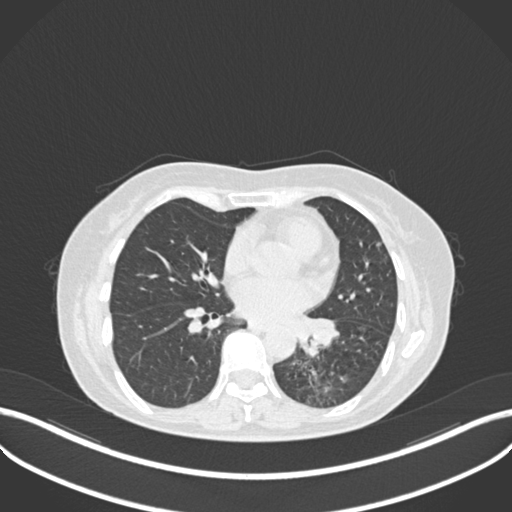
Chest CT, one axial slice; slice 120 of 270 in the series (ordered by position); reconstruction kernel B30f; 120 kVp; lung window (W 1500 / L -600 HU); 1 mm slice thickness; 512 × 512 image matrix, field of view 400 × 400 mm. Patient: female, 63 years. From the clinical record (not read from this slice): clinical TNM (as recorded): T1b N0 M0; histopathological grade: G2-3.
Structures marked on this image (bounding box drawn by a radiologist):
- lung tumour (recorded histology: adenocarcinoma): bounding box (x1, y1, x2, y2) in pixels: (295, 310, 344, 357)